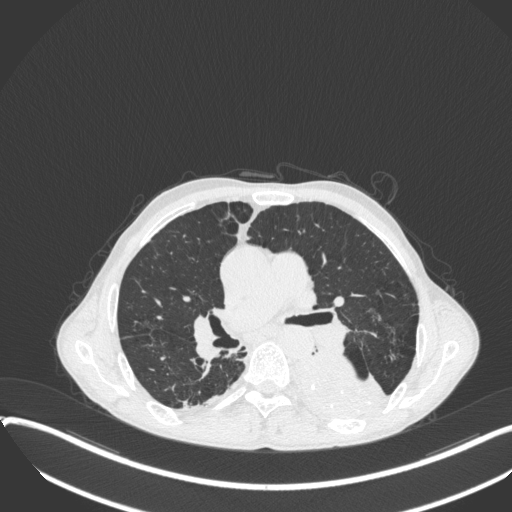
Chest CT, one axial slice. Position 219 of 400 along the scan axis. 120 kVp. Lung window (W 1500 / L -600 HU). 1 mm slice thickness. 512 × 512 image matrix, field of view 400 × 400 mm. Male patient, age 57 years. Case-level facts recorded for this patient, not image findings: clinical TNM (as recorded): T4 N0 M0.
Annotated regions visible in this slice (rectangle marked by the reading radiologist):
- lung tumour (recorded histology: squamous cell carcinoma): bounding box <285,345,395,428> (left, top, right, bottom; pixels)